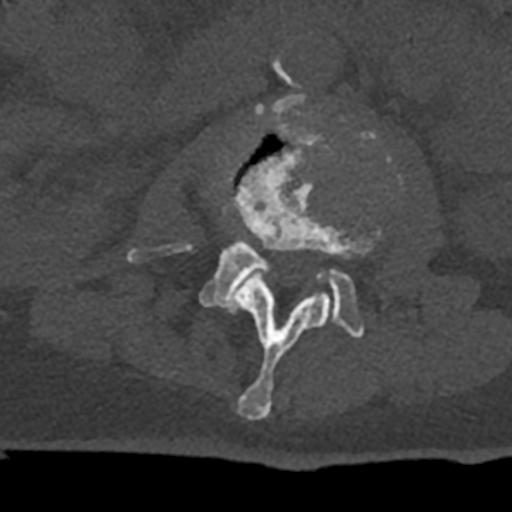
CT including the spine, one axial slice. Position 351 of 797 along the scan axis. Reconstruction kernel Br40s/3. 120 kVp. Bone window (W 1800 / L 400 HU). 0.5 mm slice thickness. 512 × 512 image matrix, field of view 160 × 160 mm. Male patient, age 74 years. Case-level facts recorded for this patient, not image findings: primary cancer: renal.
Annotated regions visible in this slice (semi-automatic segmentation, software-assisted and operator-edited):
- L2 vertebra: bounding box <218,128,381,420> (left, top, right, bottom; pixels)
- L3 vertebra: <127,94,400,338>